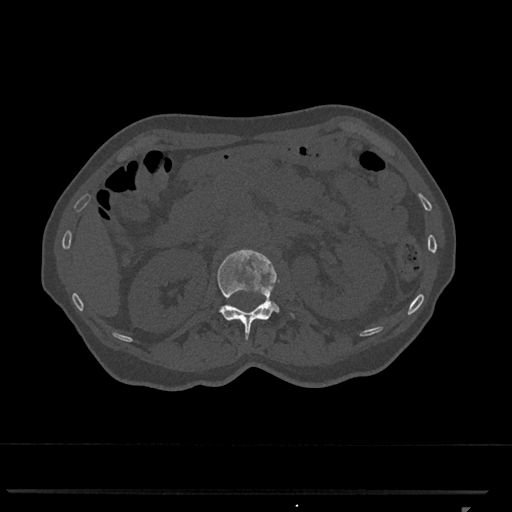
CT including the spine, one axial slice; slice 399 of 793 in the series (ordered by position); bone window (W 1800 / L 400 HU); 0.5 mm slice thickness; 512 × 512 image matrix, field of view 380 × 380 mm. Female patient, age 62 years. From the clinical record (not read from this slice): primary cancer: renal.
Outlined on this slice (semi-automatic segmentation, software-assisted and operator-edited):
- L1 vertebra: bounding box [x1, y1, x2, y2] px = [217, 250, 294, 340]